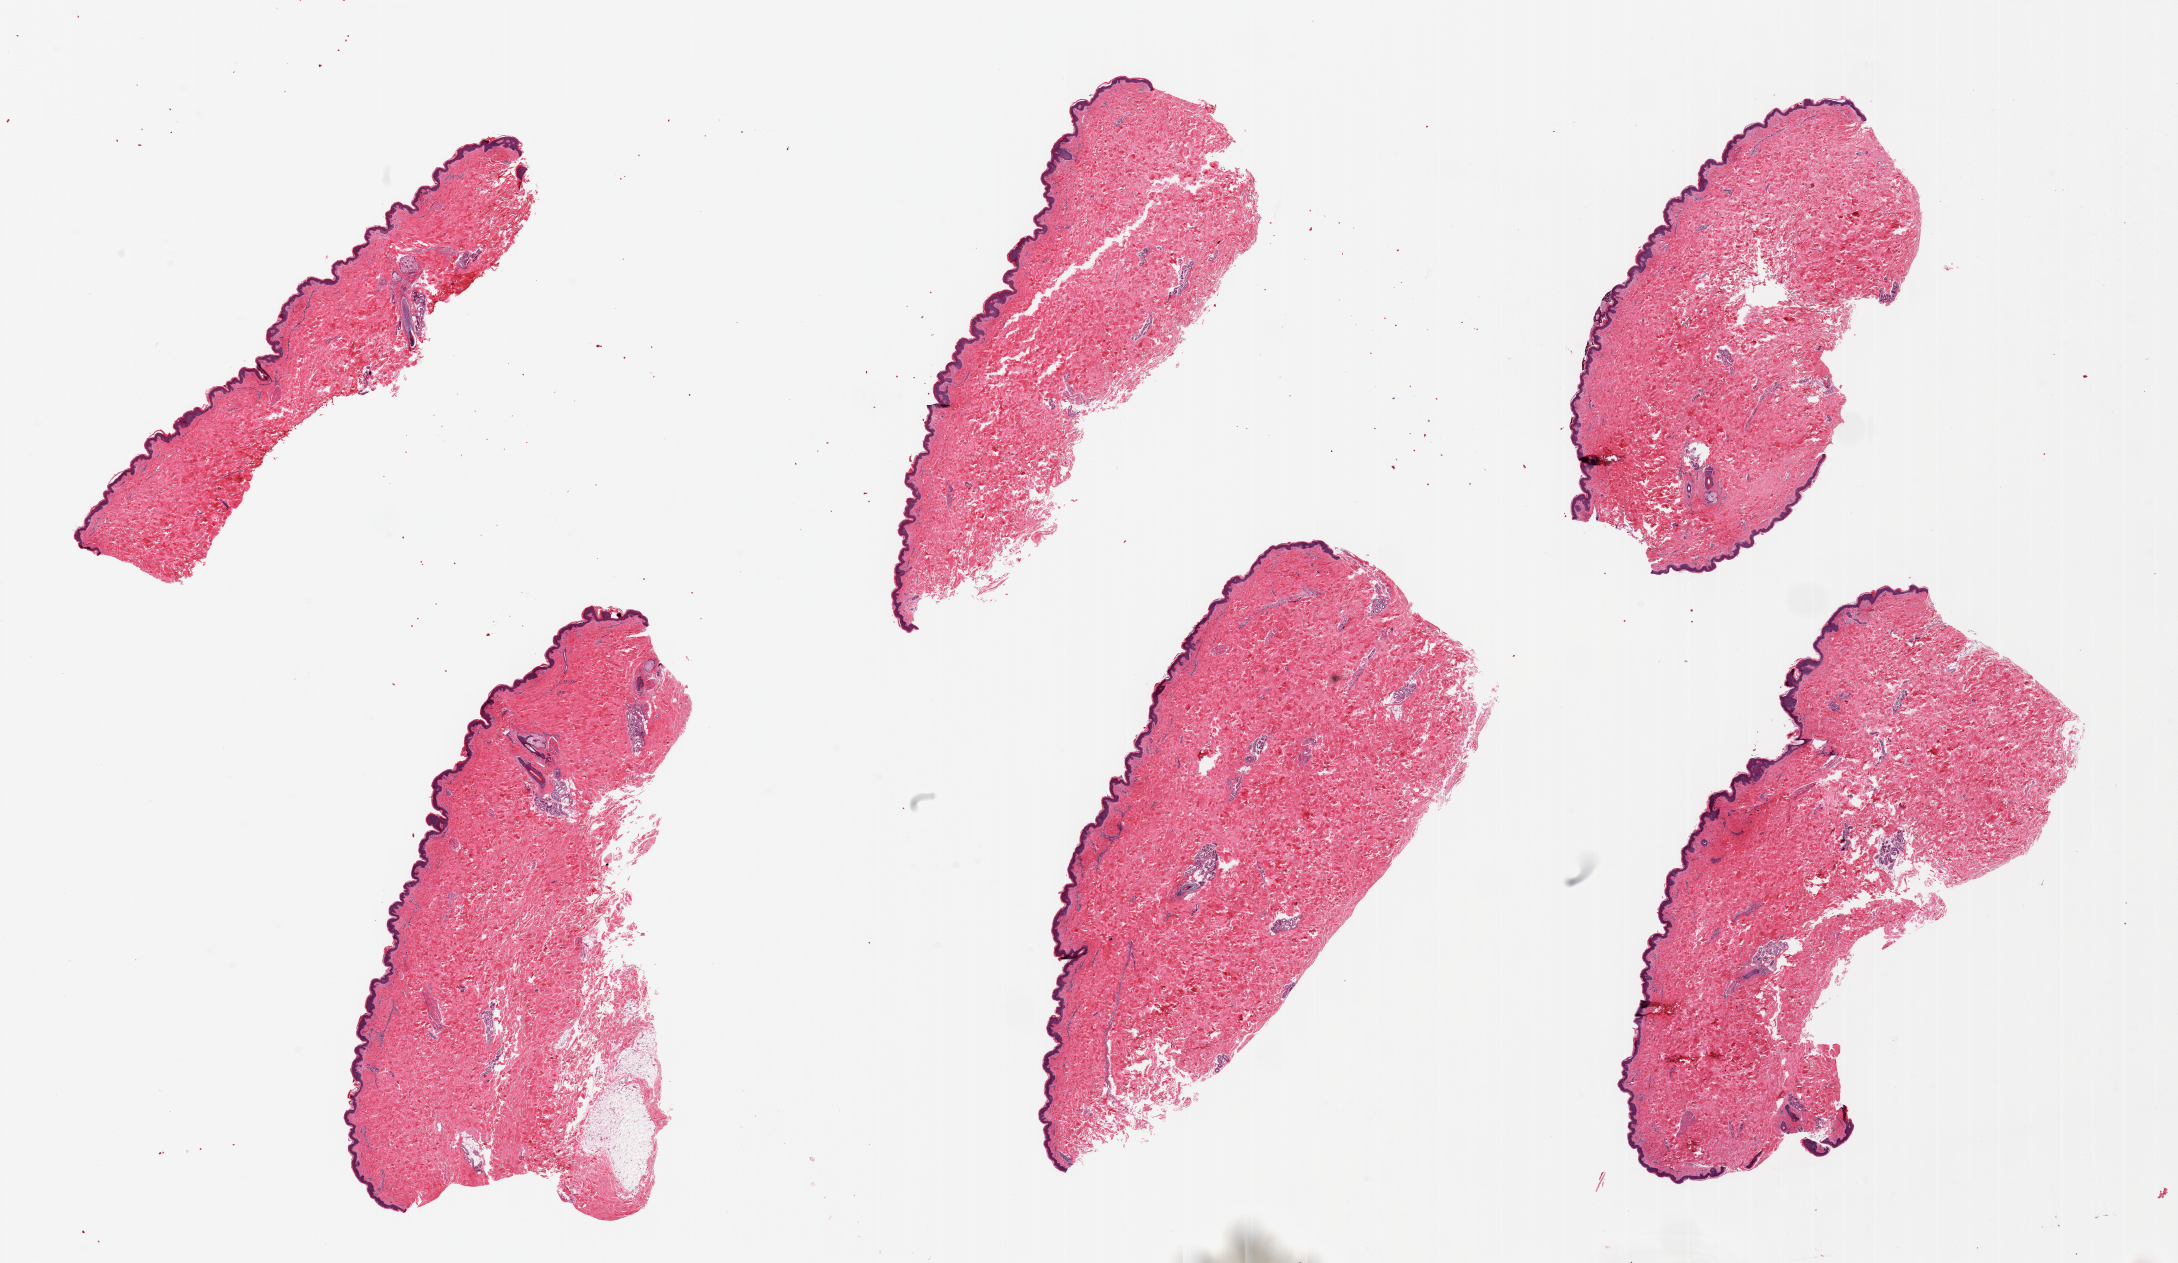
Hematoxylin and eosin (H&E) whole-slide image, brightfield, whole scanned area (about 34.5 x 20.0 mm) shown as a low-resolution overview; PAXgene-fixed paraffin-embedded (PFPE) section; sampled site (target tissue): skin of suprapubic region; donor tissue sample. Donor: male.
Reviewer comment on this tissue sample: 6 pieces ~10x5mm. Squamous epithelium is 2-3% of thickness.